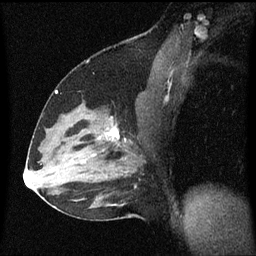
Breast MRI (dynamic contrast-enhanced), one sagittal slice; slice 36 of 60 in the series (ordered by position); dynamic contrast-enhanced series, image 2 of 3 at this slice position (ordered by acquisition); 1.5 T; TE 4.2 ms, TR 8.4 ms; 256 × 256 image matrix, field of view 200 × 200 mm. Female patient, age 37 years. From the clinical record (not read from this slice): setting: breast cancer imaged before/during neoadjuvant chemotherapy; receptor status: HR-positive, HER2-negative.
Outlined on this slice (semi-automatic segmentation, software-assisted and operator-edited):
- analysis volume of interest (the breast-tissue region the enhancement analysis was run in; not a lesion): bounding box [x1, y1, x2, y2] px = [94, 112, 141, 157]
- tumour enhancement mask (voxels above the 70 % enhancement threshold inside the analysis volume of interest): [106, 126, 120, 141]